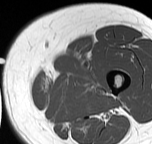
MRI of an extremity soft-tissue mass, one axial slice; slice 11 of 57 in the series (ordered by position); MR volume resampled by the dataset authors to the PET/CT grid (not the native acquisition matrix); 3.27 mm slice thickness; 152 × 144 image matrix, field of view 148 × 141 mm. Female patient. Case-level facts recorded for this patient, not image findings: histological type: pleiomorphic leiomyosarcoma; grade: intermediate; site of the primary tumour: left thigh.
Structures marked on this image (expert contour drawn on MRI and transferred to this co-registered scan by the dataset authors):
- gross tumour volume including surrounding oedema: box from (x=43, y=71) to (x=103, y=95) px